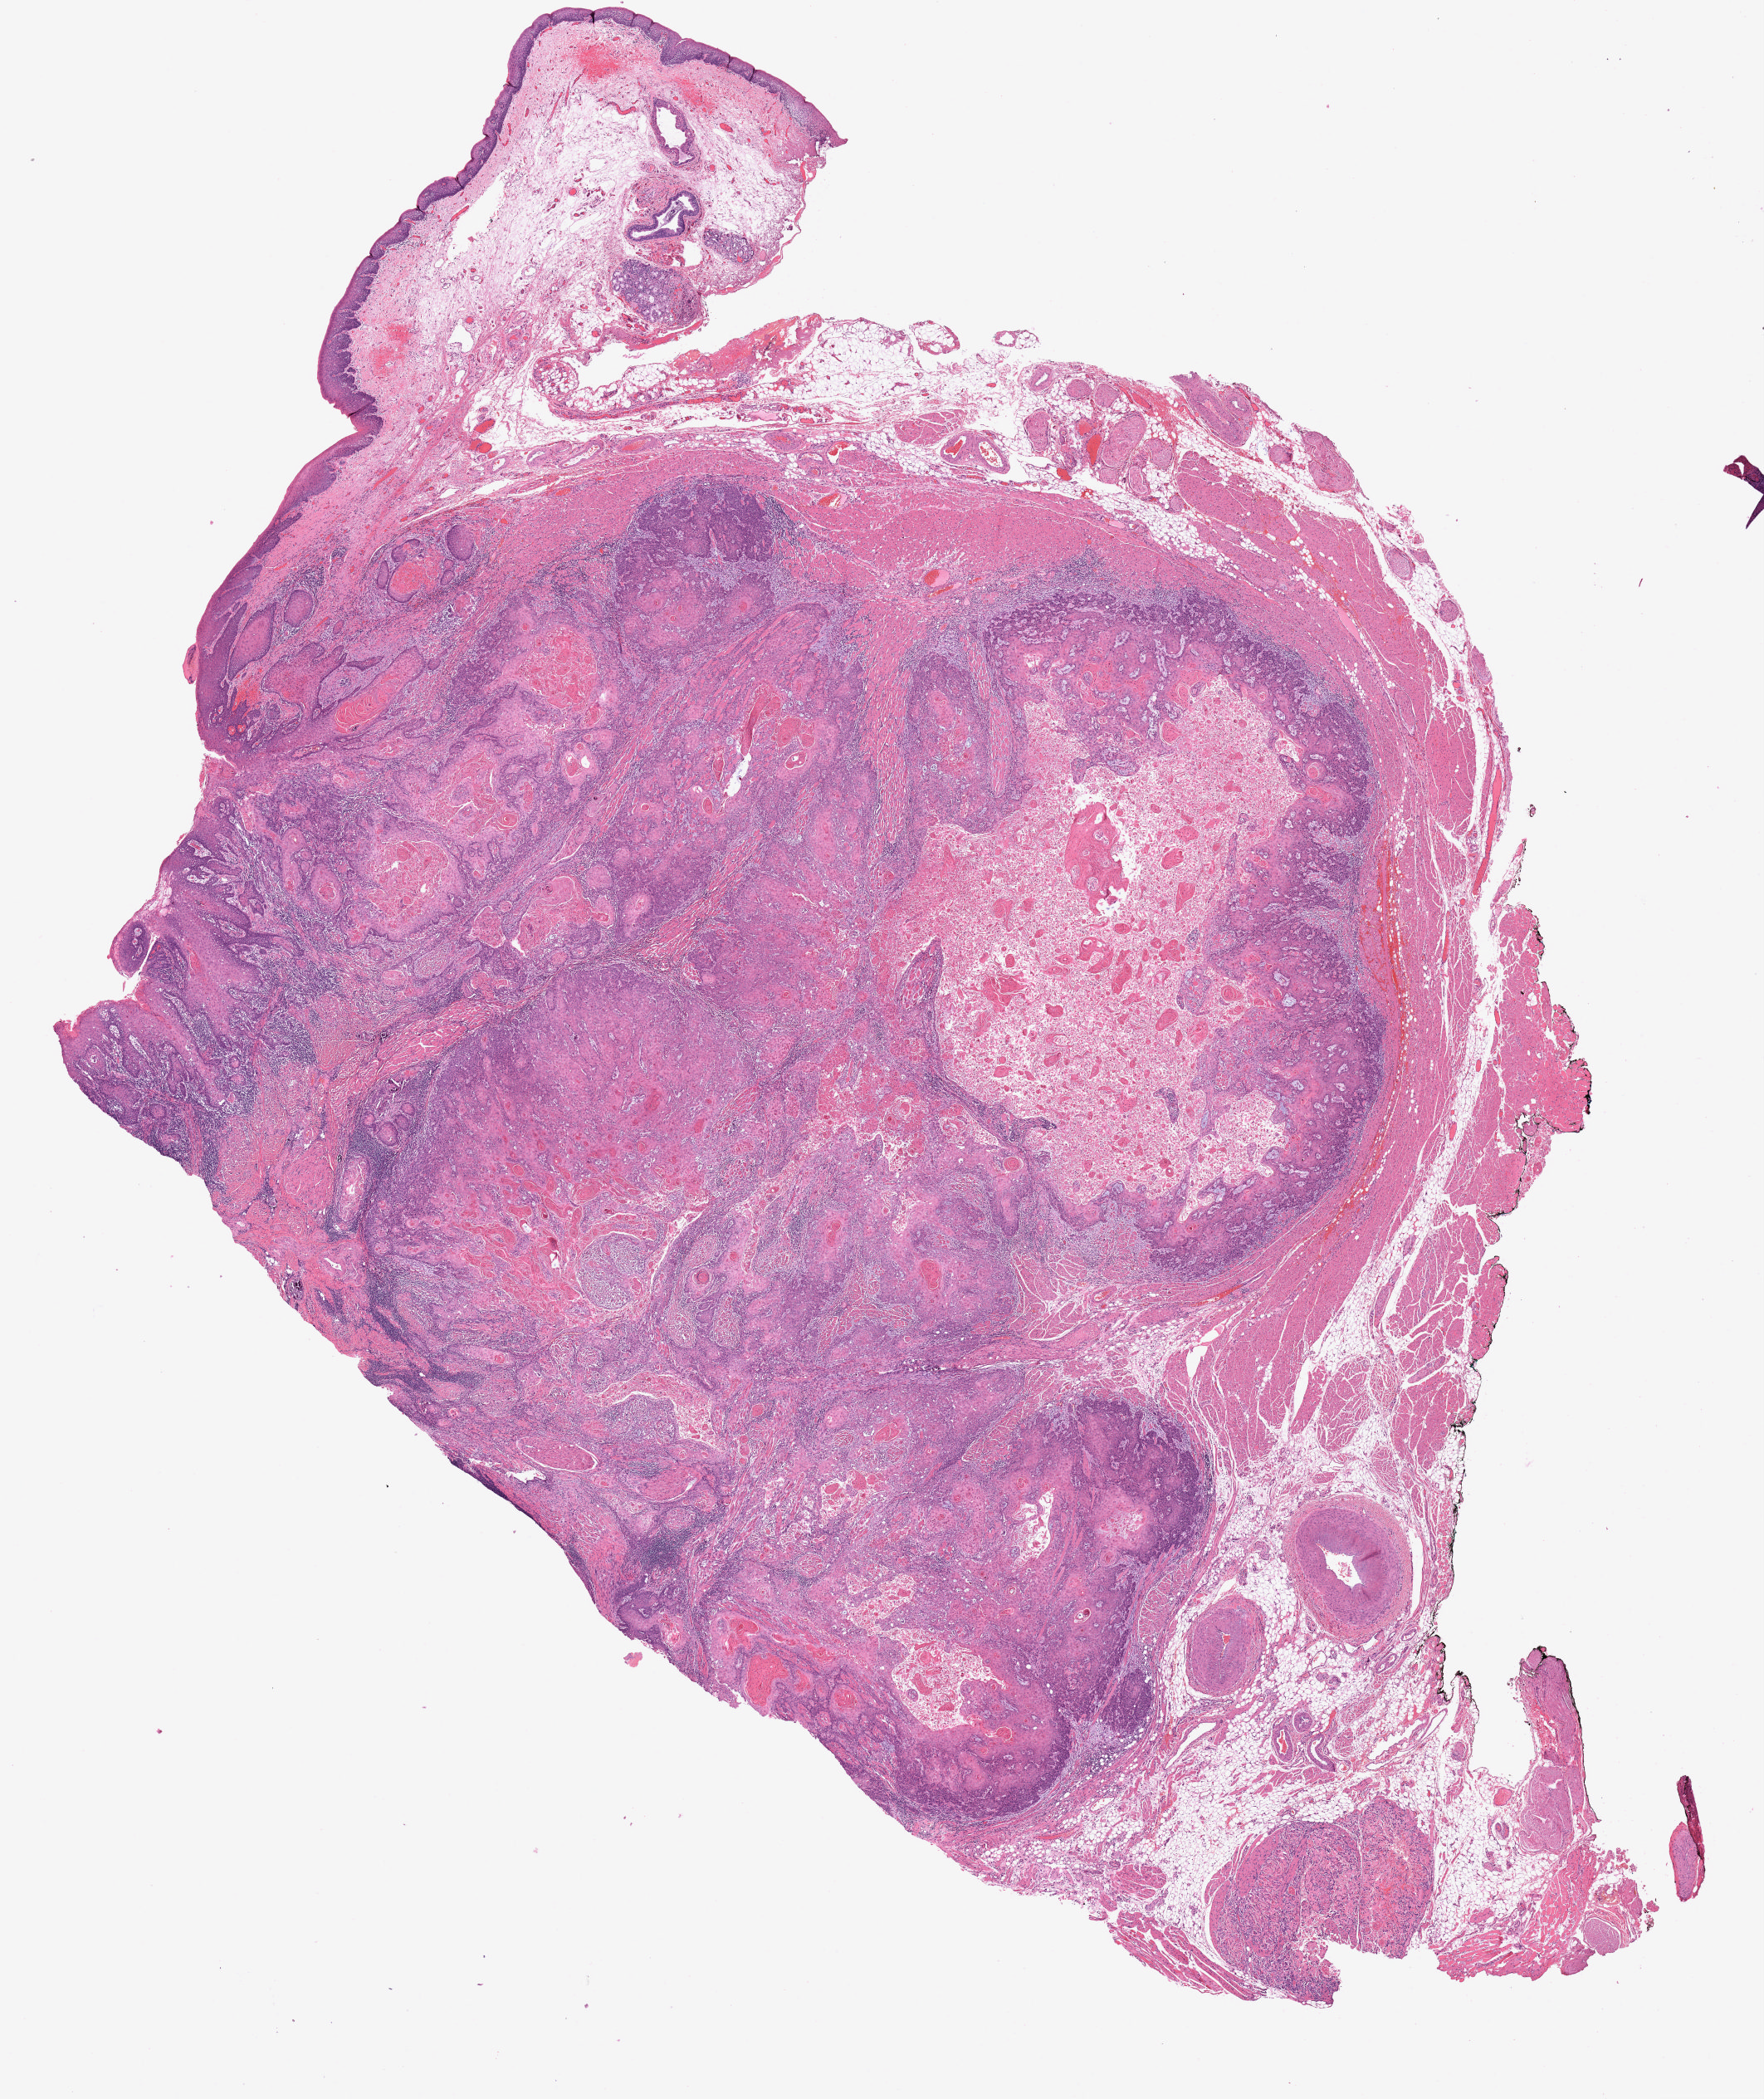
Digitized H&E tissue section (whole slide) — low-resolution overview of the scanned area, about 17.0 x 20.2 mm (from a 20x scan). Formalin-fixed paraffin-embedded (FFPE) diagnostic section. Head and neck, primary tumour sample. Female, age 85 years at initial diagnosis. Histologic grade: G2 (moderately differentiated).
Diagnosis: Squamous cell carcinoma, NOS (tongue, NOS). AJCC pathologic stage: I. TNM: T1 N0 MX.